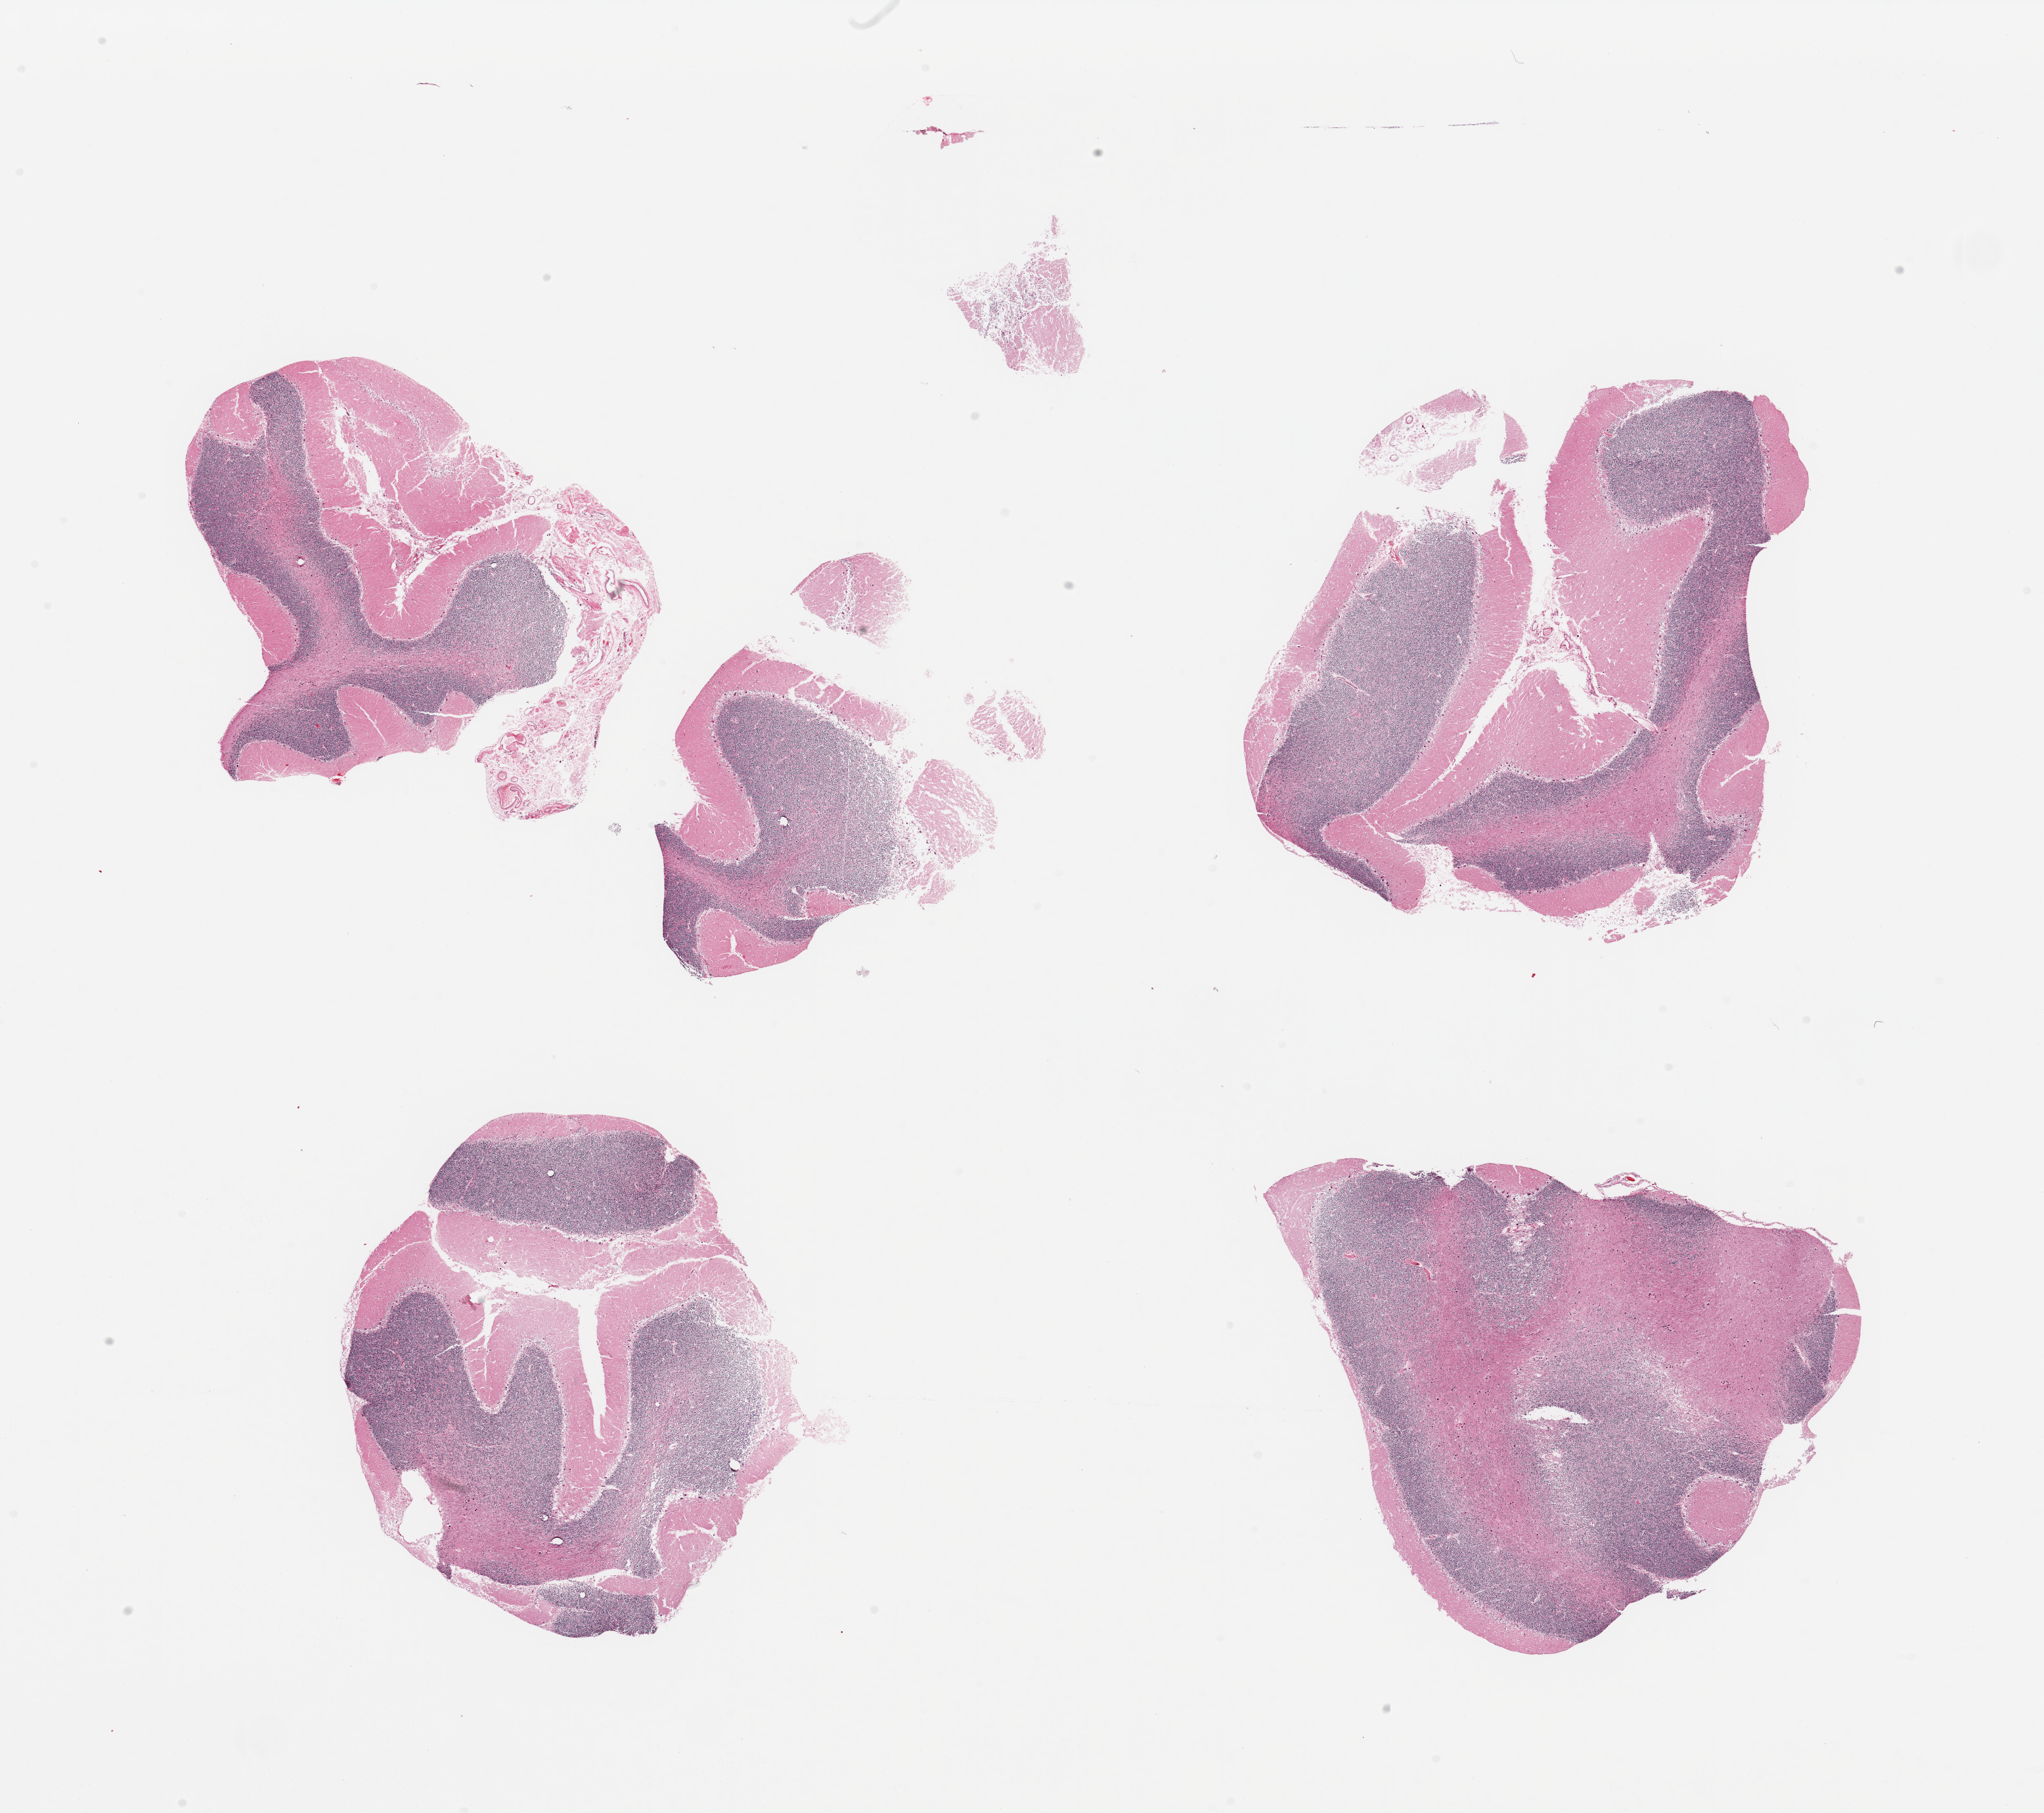
Whole-slide image, haematoxylin and eosin stain, whole scanned area (about 24.6 x 21.8 mm, acquisition: 20x scan) shown as a low-resolution overview. PAXgene-fixed, paraffin-embedded tissue. Sampled site (target tissue): cerebellum. Tissue donor sample. Donor: male.
• reviewer comment on this tissue sample: 5 fragmented pieces; meninges present